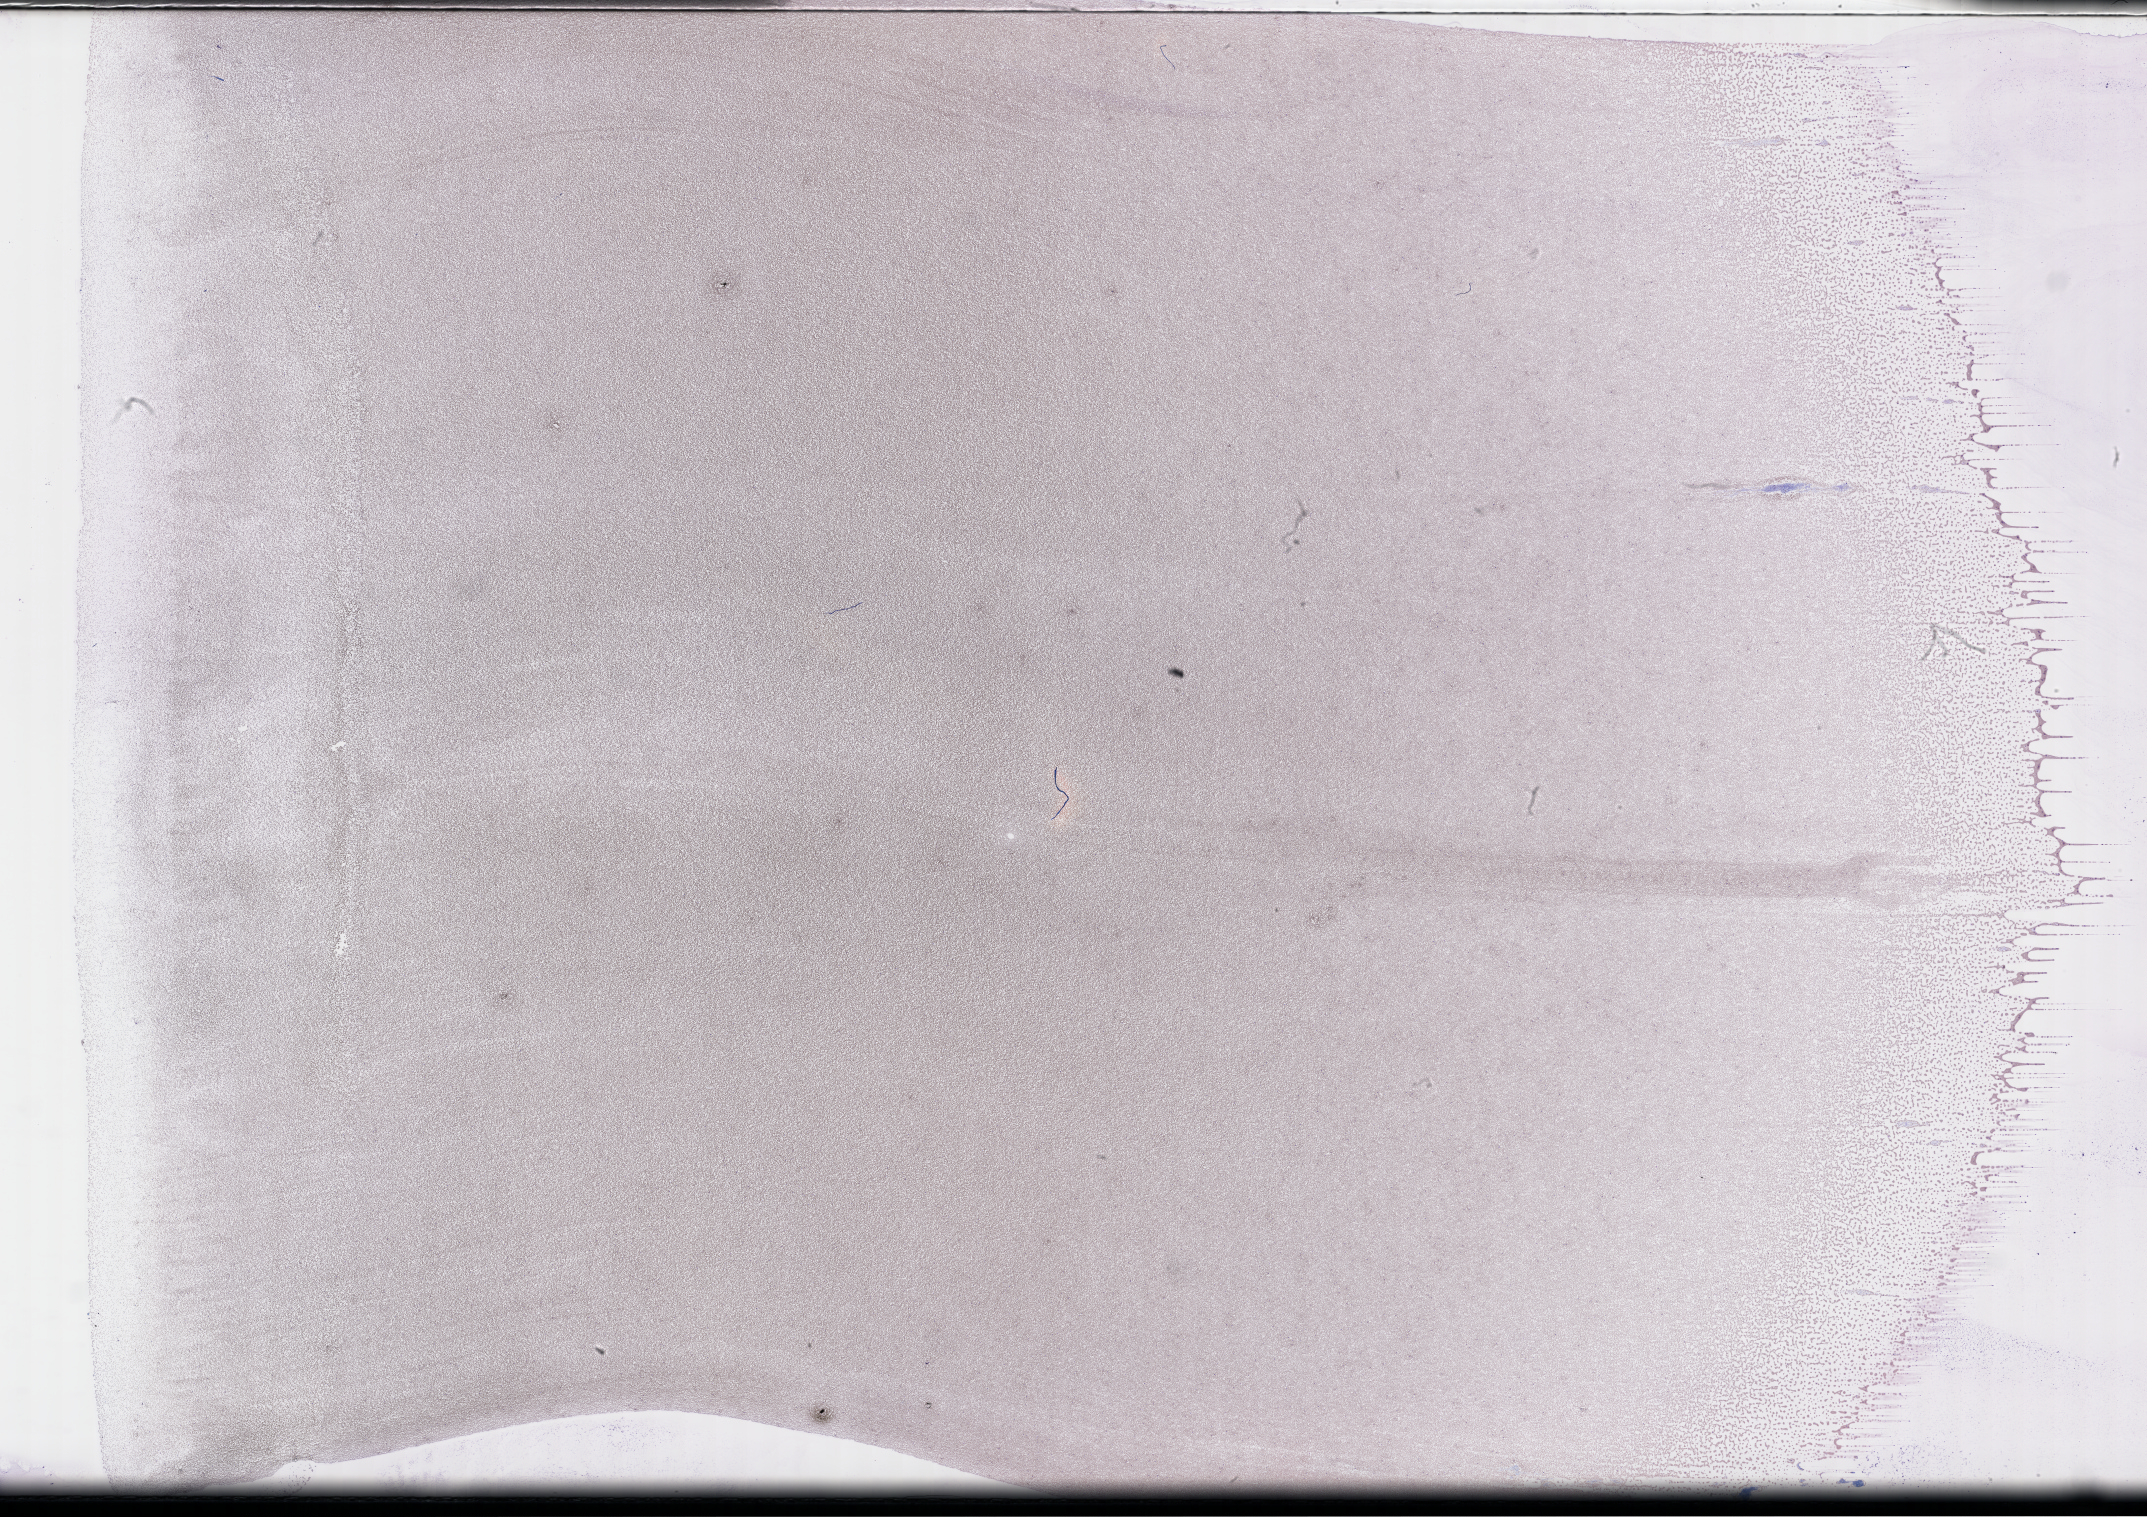
Wright–Giemsa-stained whole blood smear, whole-slide image — a low-resolution overview of the entire scanned area, about 34.7 x 24.5 mm, smear from an EDTA sample. Male patient.
Patient diagnosis: Plasma Cell Myeloma.